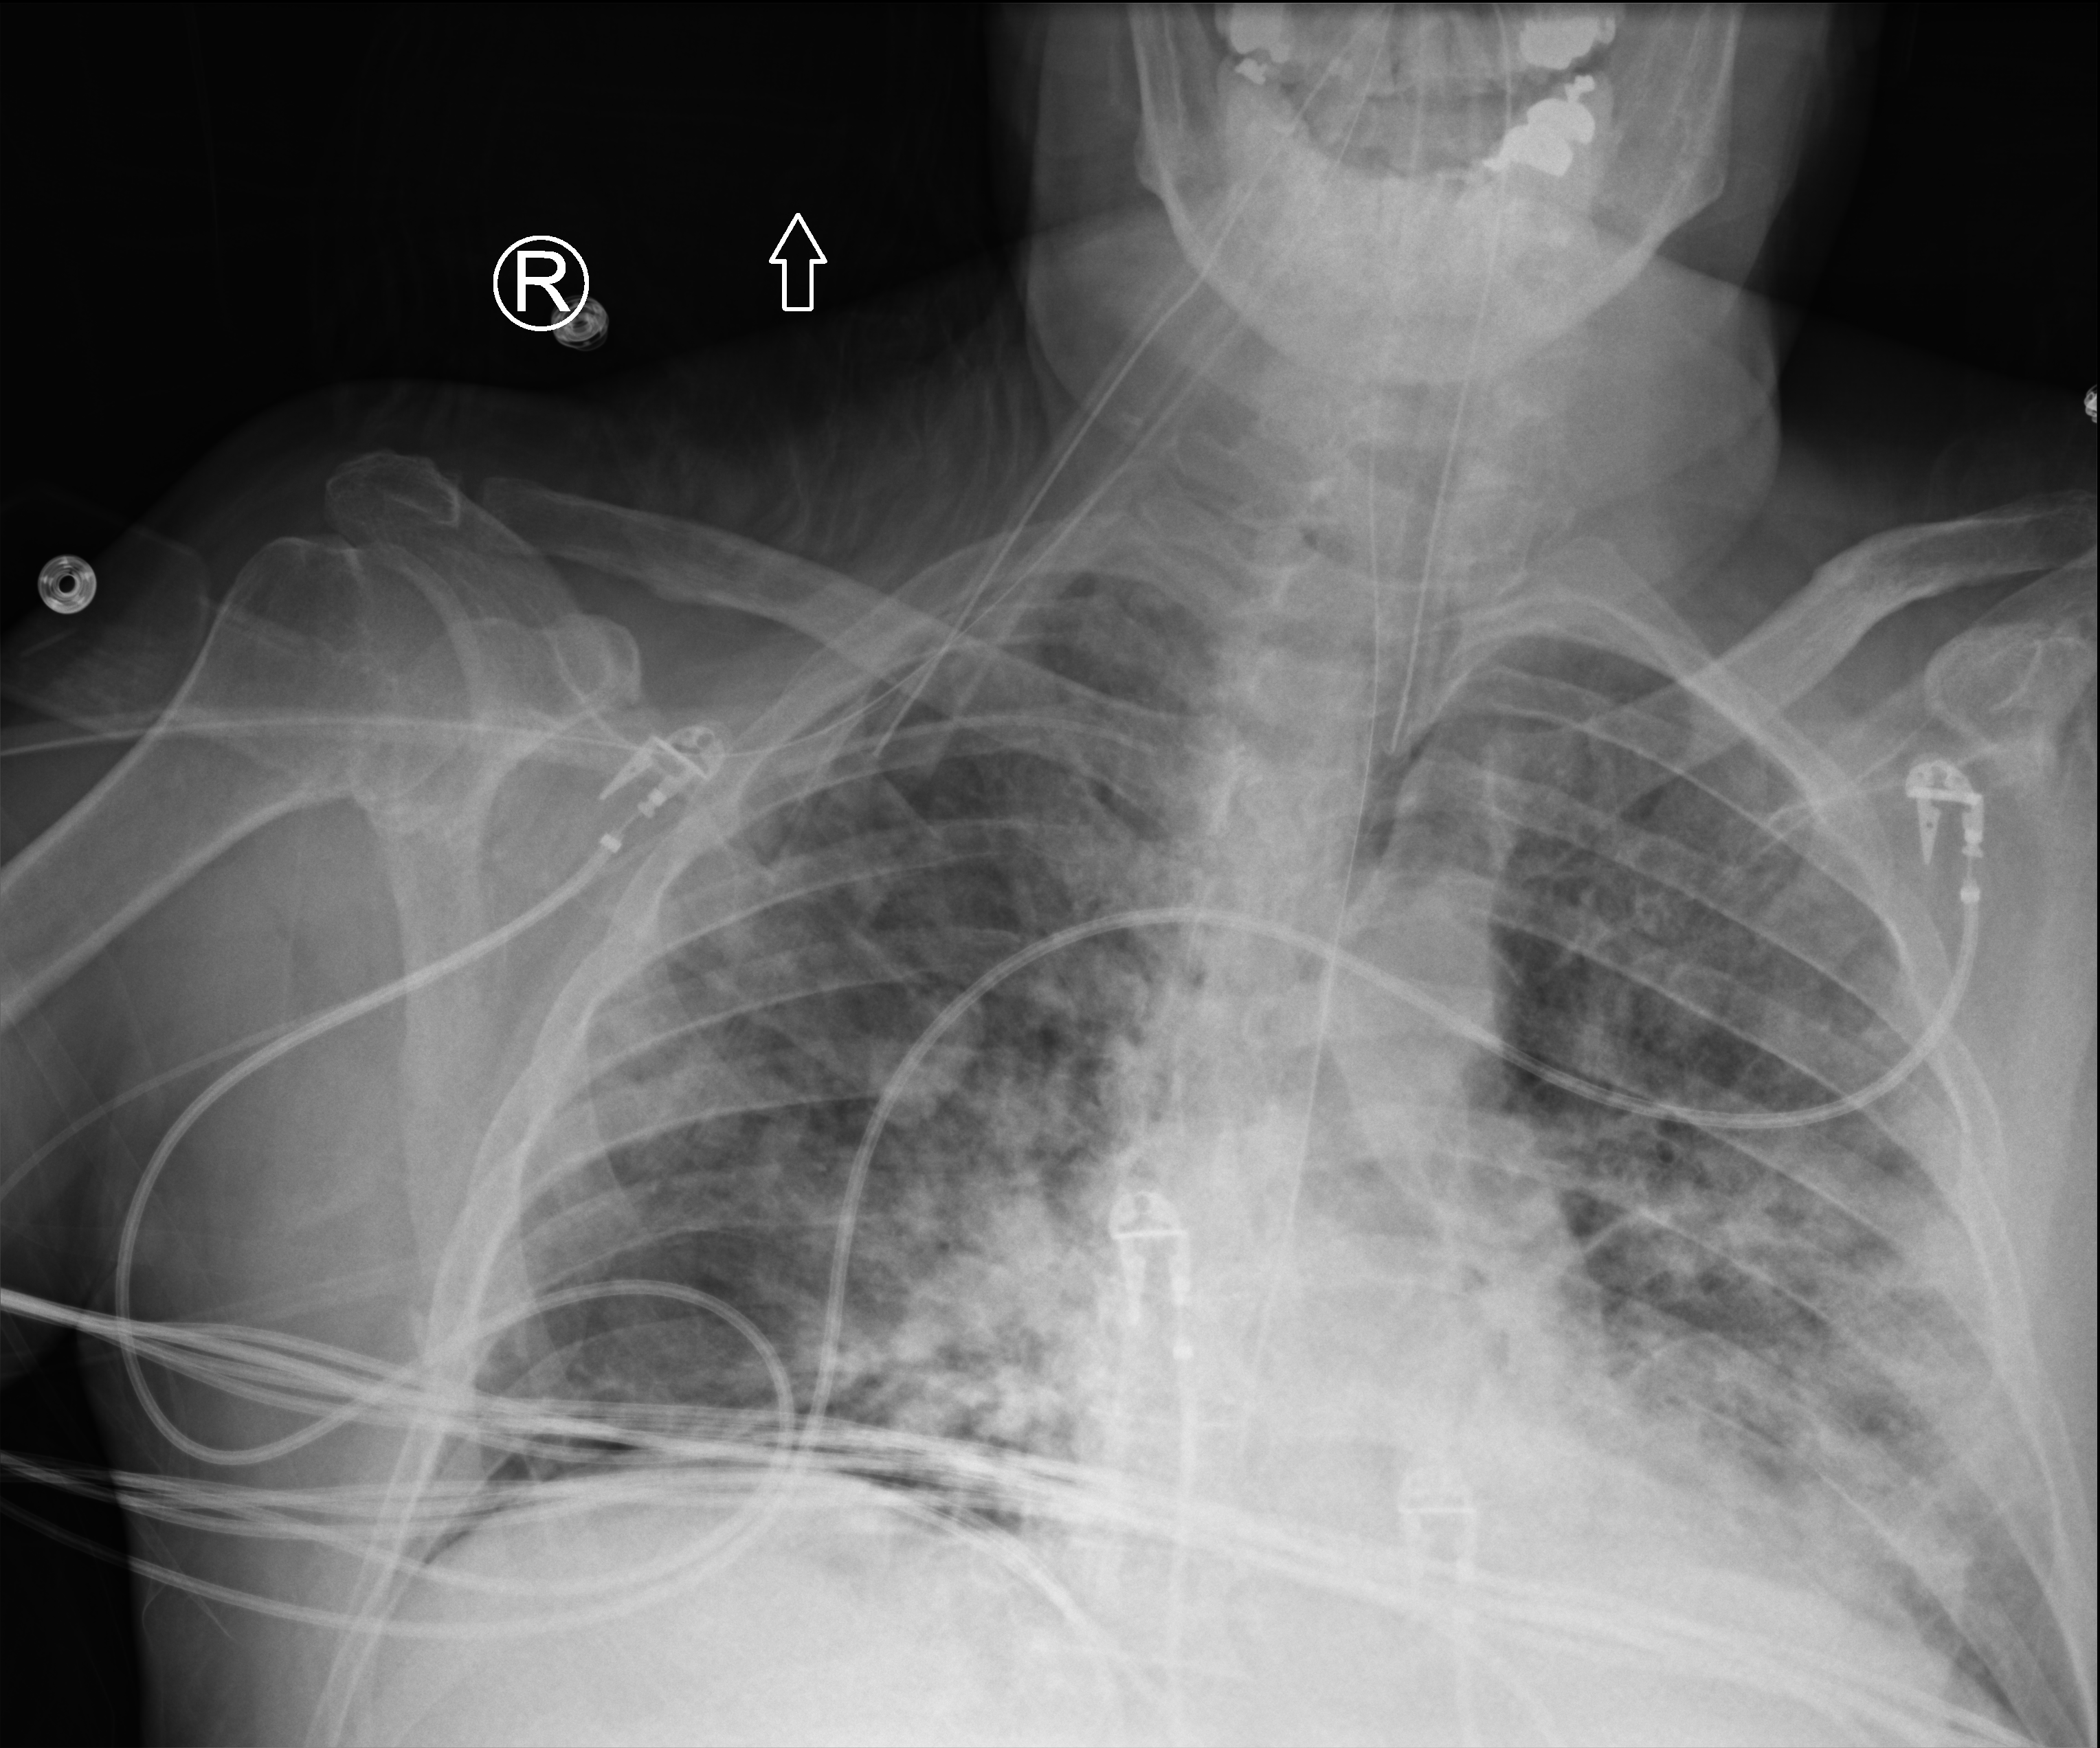
Bedside chest radiograph (computed radiography), anteroposterior (AP) projection. Male patient hospitalised with COVID-19, age 60–74 years.
Hospital-stay facts (about this admission, not read from this image; timing relative to this image not recorded):
- admitted to intensive care during this hospital stay: yes
- COPD (admission record): no